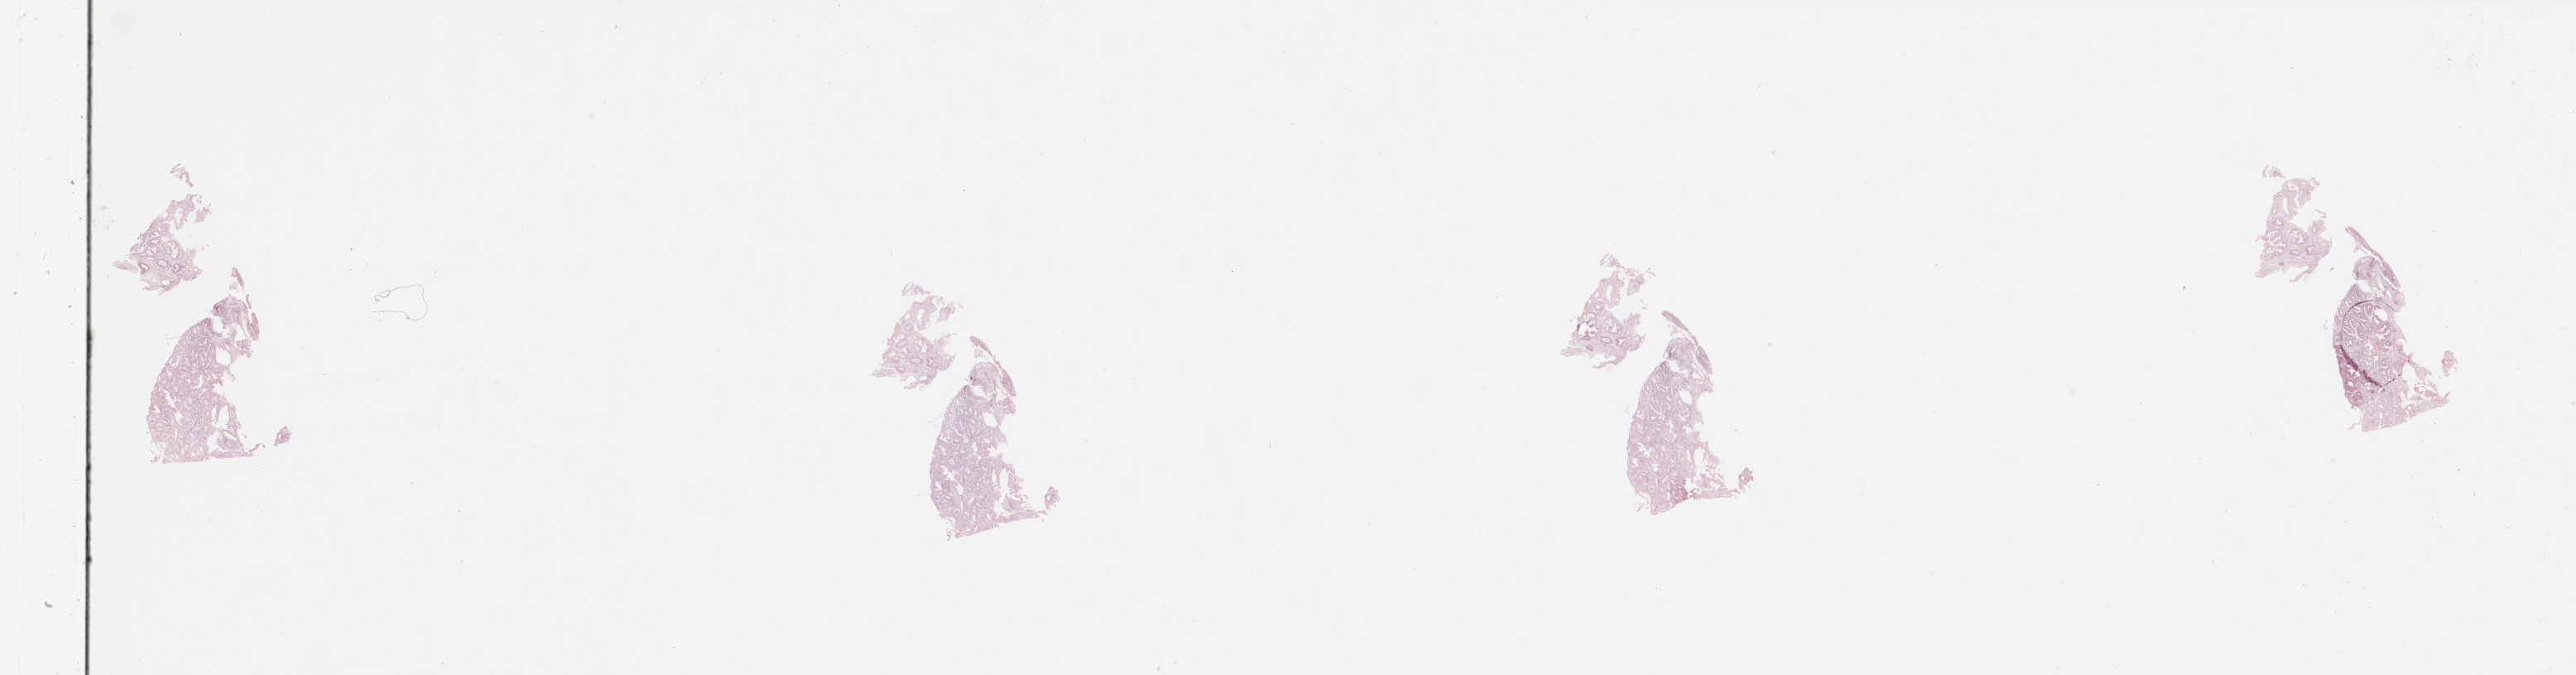
Digitized H&E tissue section (whole slide) — a low-resolution overview of the entire scanned area, about 49.2 x 12.9 mm, tumour tissue sample, sampled site: uterus. Female, 67 y/o. Histologic grade: G1 (well differentiated). Slide review estimates, as recorded: tumour nuclei 80%, necrosis 2%.
Primary tumour site (as recorded): anterior endometrium. AJCC pathologic stage: I. Histologic diagnosis: Endometrioid adenocarcinoma, NOS.